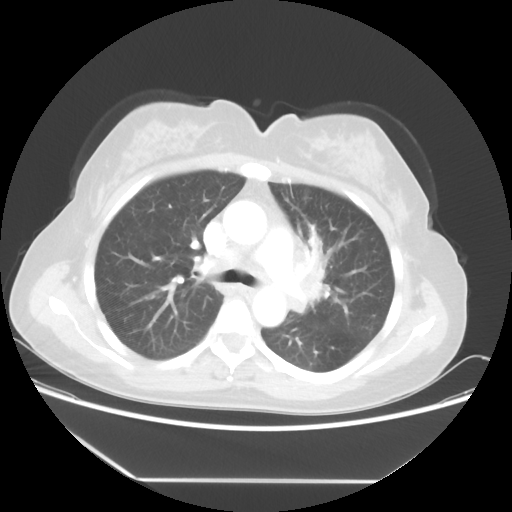
Chest CT, one axial slice. Position 34 of 52 along the scan axis. 100 kVp. Lung window (W 1500 / L -600 HU). 5 mm slice thickness. 512 × 512 image matrix, field of view 390 × 390 mm. Patient: female, 50 years. From the clinical record (not read from this slice): clinical TNM (as recorded): T2 N3 M0.
Structures marked on this image (bounding box drawn by a radiologist):
- lung tumour (recorded histology: adenocarcinoma): box from (x=292, y=228) to (x=338, y=324) px